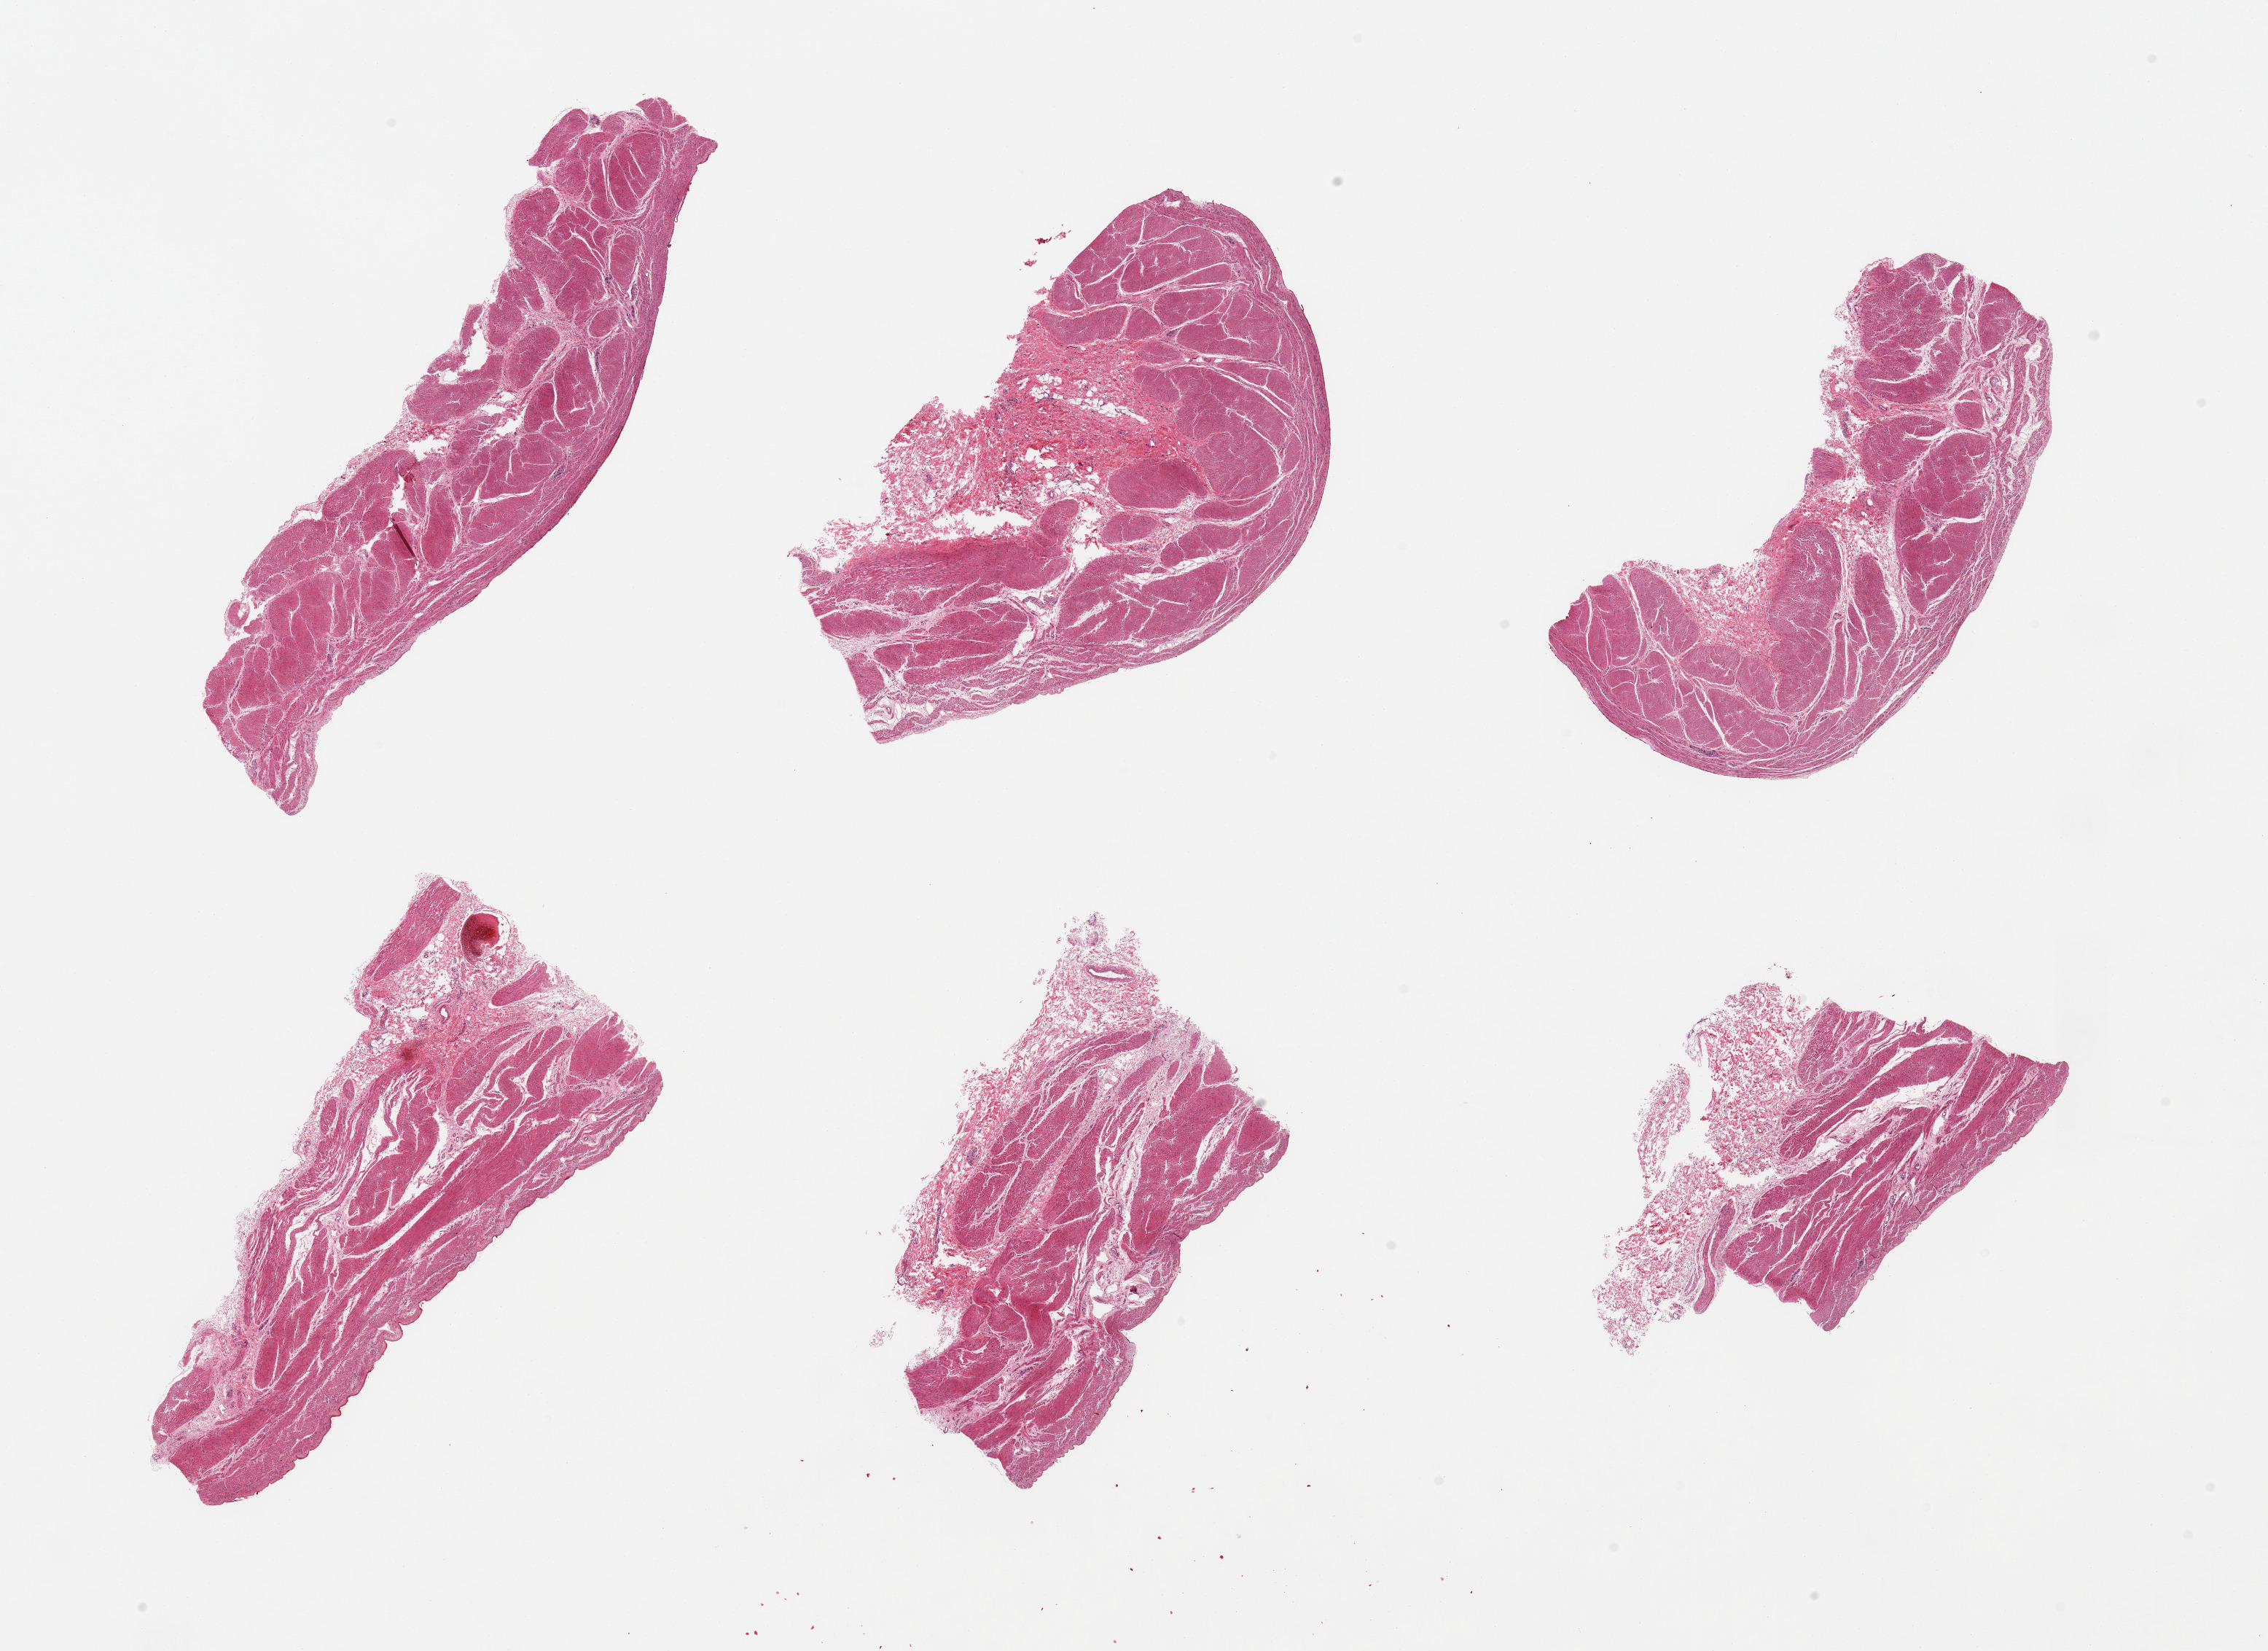
Hematoxylin and eosin (H&E) whole-slide image, whole scanned area (about 24.6 x 17.9 mm) shown as a low-resolution overview. PAXgene-fixed, paraffin-embedded tissue. Section of stomach (target tissue). Donor tissue sample. Male donor.
- reviewer comment on this tissue sample: 6 pieces, mucosa completely autolyzed/sloughed